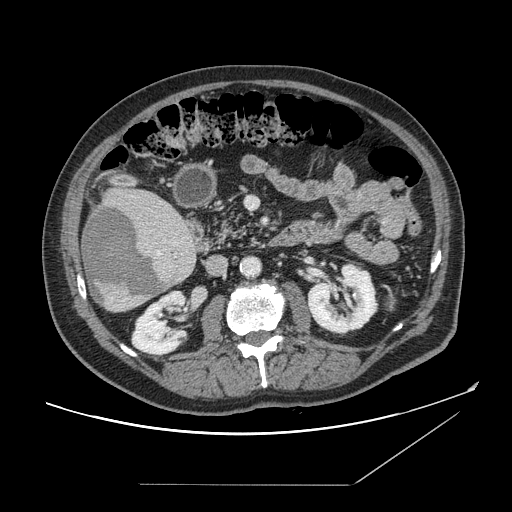
Contrast-enhanced abdominal CT, one axial slice. Position 62 of 166 along the scan axis. Intravenous contrast given. Soft-tissue window (W 400 / L 40 HU). 512 × 512 image matrix, field of view 416 × 416 mm. Male patient, age 80 years. From the clinical record (not read from this slice): diagnosis: colorectal cancer liver metastases, imaged before liver resection; multiple liver metastases: no; largest metastasis: 2.2 cm; chemotherapy before resection: no.
Outlined on this slice (manually delineated by an expert):
- liver: bounding box [x1, y1, x2, y2] px = [81, 188, 198, 313]
- planned liver remnant (the part of the liver to remain after resection): [130, 189, 171, 209]
- liver metastasis: [84, 205, 167, 305]